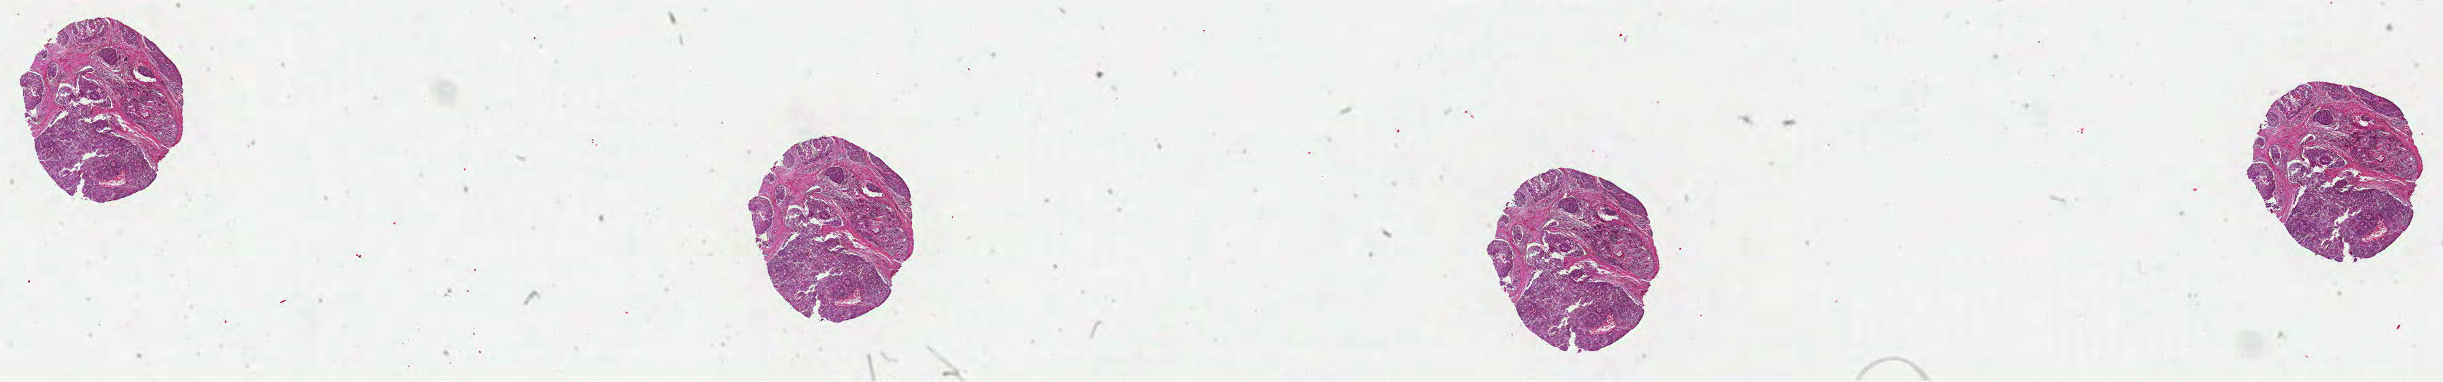
Digitized Hematoxylin and eosin (H&E) stained tissue section (whole slide), low-resolution overview of the scanned area, about 39.6 x 6.2 mm (from a 40x scan), formalin-fixed paraffin-embedded (FFPE) diagnostic section, sample: primary tumour, head and neck. Patient: male, age at initial diagnosis 82 years. Histologic grade: G2 (moderately differentiated).
• laterality: right
• lymph nodes positive (case pathology): 2 of 15 examined
• pathologic diagnosis: Squamous cell carcinoma, NOS (overlapping lesion of lip, oral cavity and pharynx)
• AJCC pathologic stage: IVA